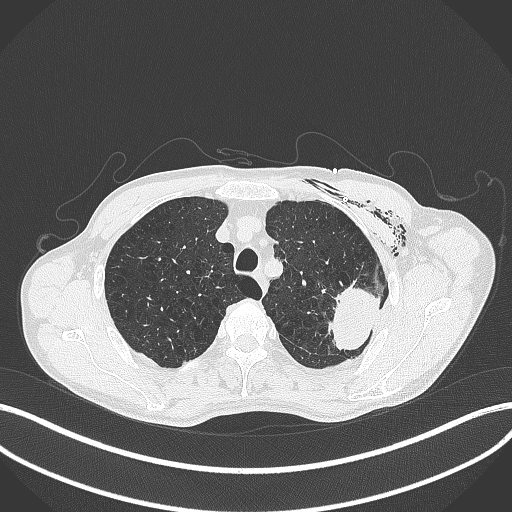
Chest CT, one axial slice; slice 330 of 457 in the series (ordered by position); reconstruction kernel B70f; lung window (W 1500 / L -600 HU); 1 mm slice thickness; 512 × 512 image matrix, field of view 400 × 400 mm. Male patient, age 58 years. Case-level facts recorded for this patient, not image findings: clinical TNM (as recorded): T3 N0 M0.
Annotated regions visible in this slice (bounding box drawn by a radiologist):
- lung tumour (recorded histology: adenocarcinoma): bounding box <327,278,383,352> (left, top, right, bottom; pixels)